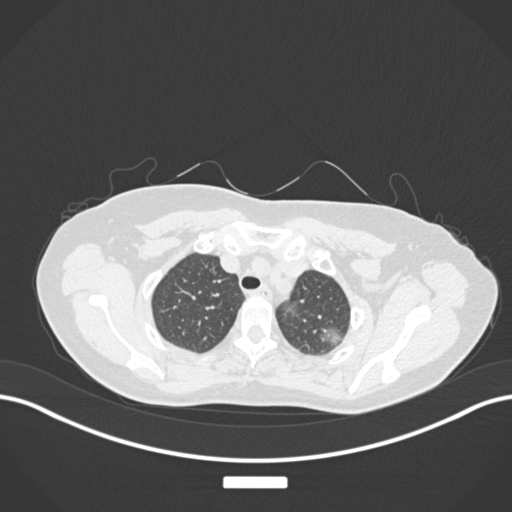
Chest CT, one axial slice; slice 143 of 181 in the series (ordered by position); 120 kVp; lung window (W 1500 / L -600 HU); 1 mm slice thickness; 512 × 512 image matrix, field of view 400 × 400 mm. Patient: female, 58 years. From the clinical record (not read from this slice): clinical TNM (as recorded): T1c N0 M0.
Annotated regions visible in this slice (bounding box drawn by a radiologist):
- lung tumour (recorded histology: adenocarcinoma): bounding box <317,323,348,351> (left, top, right, bottom; pixels)